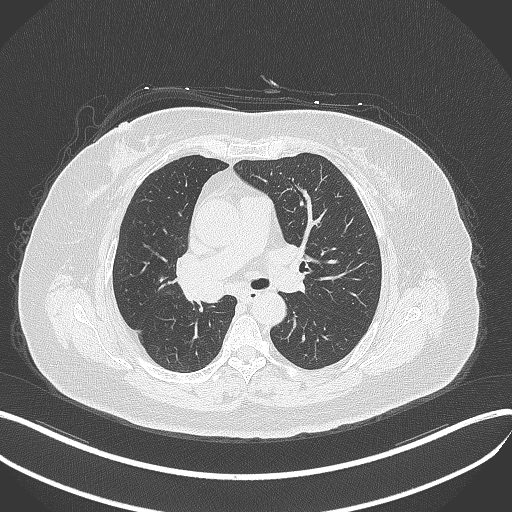
Chest CT, one axial slice. Slice 214 of 376 in the series (ordered by position). Lung window (W 1500 / L -600 HU). 512 × 512 image matrix, field of view 400 × 400 mm. Female patient, age 60 years. From the clinical record (not read from this slice): clinical TNM (as recorded): T1c N0 M0.
Outlined on this slice (rectangle marked by the reading radiologist):
- lung tumour (recorded histology: squamous cell carcinoma): bounding box <179,275,227,304> (left, top, right, bottom; pixels)